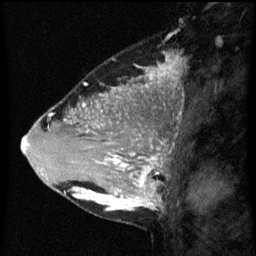
Breast MRI (dynamic contrast-enhanced), one sagittal slice; slice 23 of 60 in the series (ordered by position); dynamic contrast-enhanced series, image 2 of 3 at this slice position (ordered by acquisition); 1.5 T; TE 4.2 ms, TR 8 ms; 2.3 mm slice thickness; 256 × 256 image matrix, field of view 180 × 180 mm. Female patient, age 33 years.
Outlined on this slice (semi-automatic segmentation, software-assisted and operator-edited):
- analysis volume of interest (the breast-tissue region the enhancement analysis was run in; not a lesion): bounding box [x1, y1, x2, y2] px = [71, 118, 169, 211]
- tumour enhancement mask (voxels above the 70 % enhancement threshold inside the analysis volume of interest): [73, 126, 163, 211]